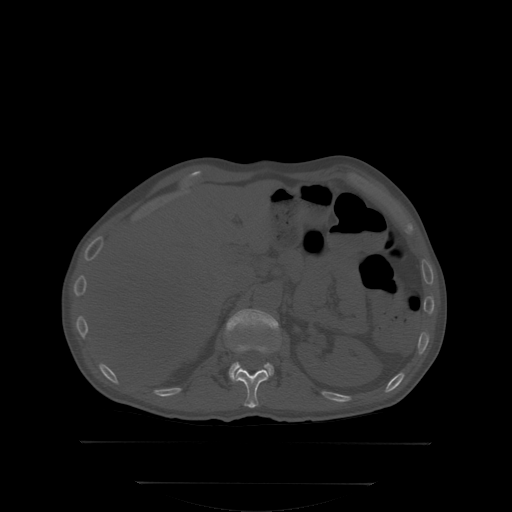
CT including the spine, one axial slice. Bone window (W 1800 / L 400 HU). 512 × 512 image matrix, field of view 500 × 500 mm. Male patient, age 58 years. Case-level facts recorded for this patient, not image findings: primary cancer: prostate; vertebrae with lytic lesions (as recorded): L1.
Annotated regions visible in this slice (semi-automatically segmented with operator editing):
- L1 vertebra: bounding box (x1, y1, x2, y2) in pixels: (227, 309, 279, 379)
- T12 vertebra: (234, 344, 273, 408)